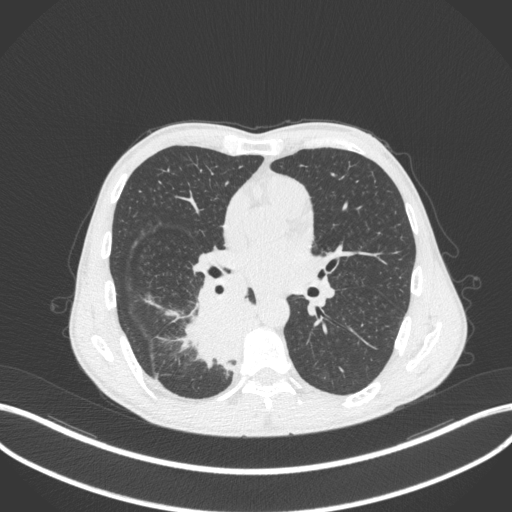
Chest CT, one axial slice; slice 193 of 371 in the series (ordered by position); reconstruction kernel B31f; 120 kVp; lung window (W 1500 / L -600 HU); 512 × 512 image matrix. Patient: male, 58 years. From the clinical record (not read from this slice): clinical TNM (as recorded): T3 N1 M1.
Outlined on this slice (bounding box drawn by a radiologist):
- lung tumour (recorded histology: squamous cell carcinoma): bounding box [x1, y1, x2, y2] px = [179, 284, 265, 371]